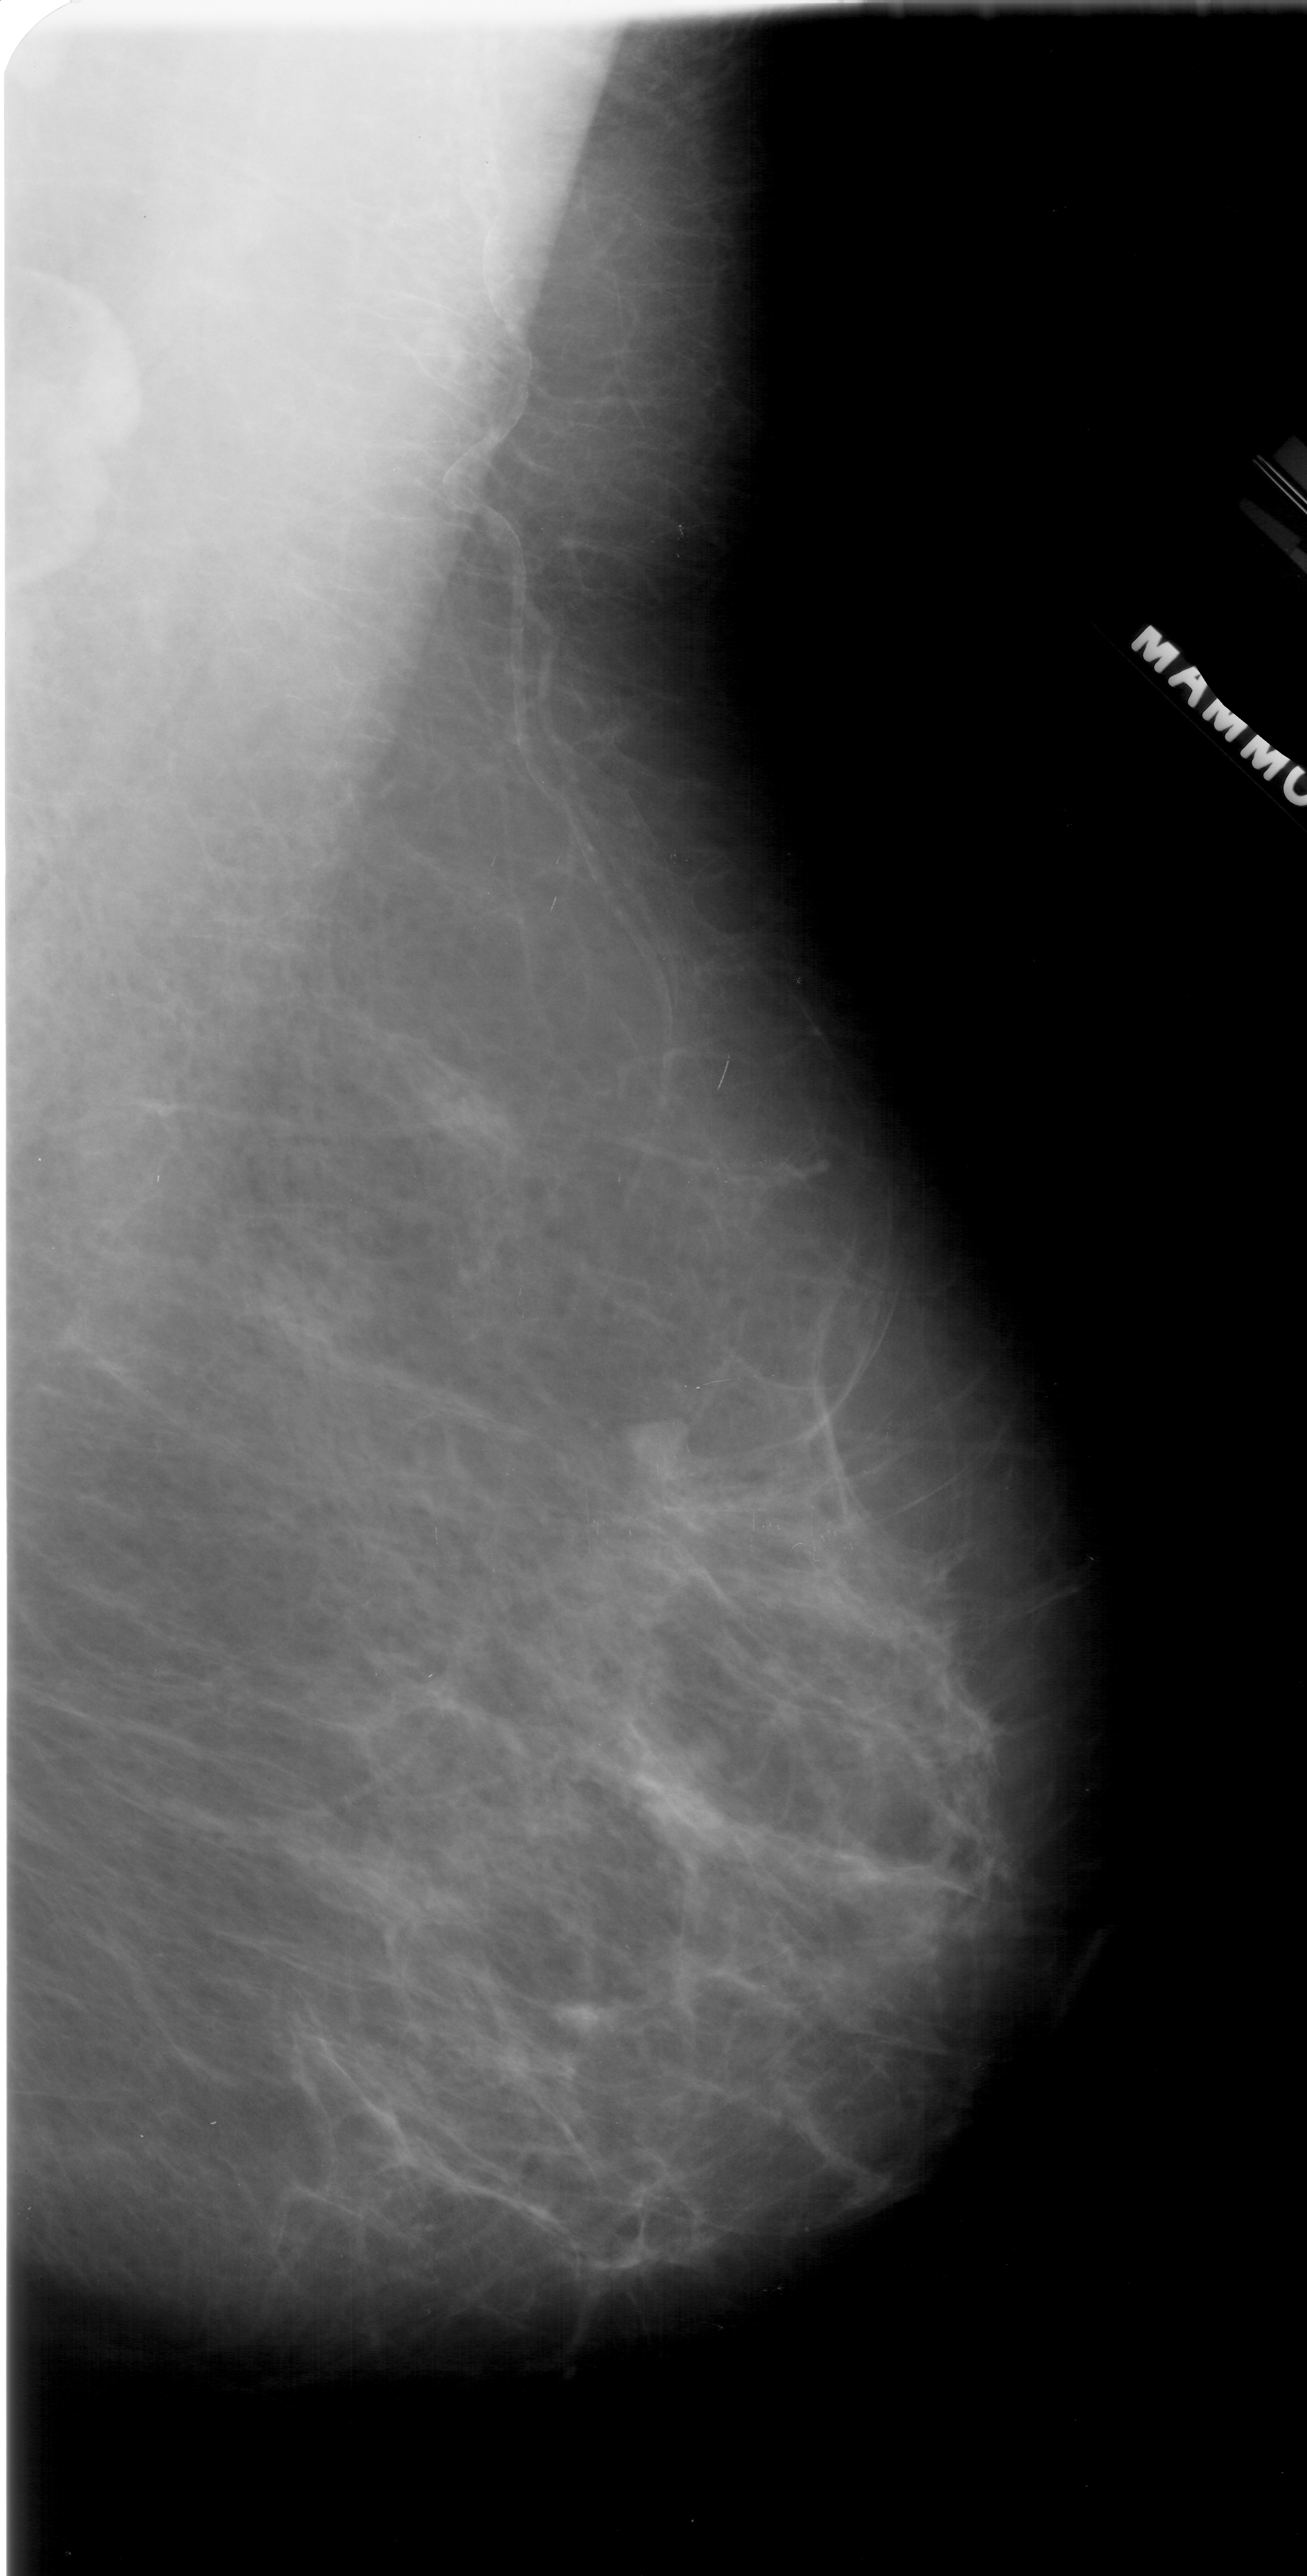
Scanned film-screen mammogram, right breast, MLO view, BI-RADS breast density category 2 (scale 1–4).
Mass, shape lobulated, margins obscured; BI-RADS assessment category 4; subtlety rating 2 on a 1 (subtle) to 5 (obvious) scale; pathology result (as recorded, not read from the image): malignant.